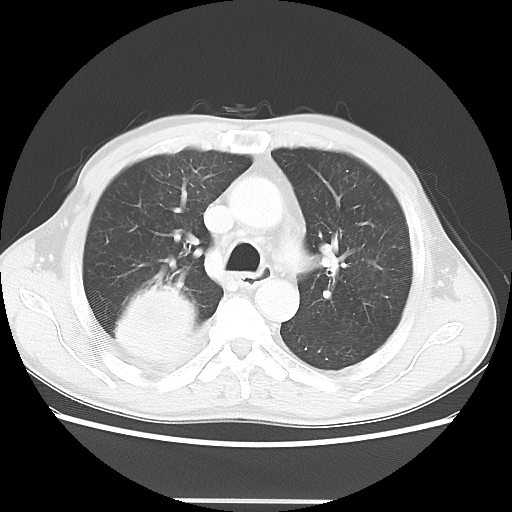
Chest CT, one axial slice; slice 34 of 48 in the series (ordered by position); reconstruction kernel LUNG; 100 kVp; lung window (W 1500 / L -600 HU); 5 mm slice thickness; 512 × 512 image matrix, field of view 361 × 361 mm. Patient: male, 66 years. From the clinical record (not read from this slice): clinical TNM (as recorded): T4 N1 M1; histopathological grade: G3.
Structures marked on this image (rectangle marked by the reading radiologist):
- lung tumour (recorded histology: small cell carcinoma): bounding box [x1, y1, x2, y2] px = [103, 277, 203, 374]